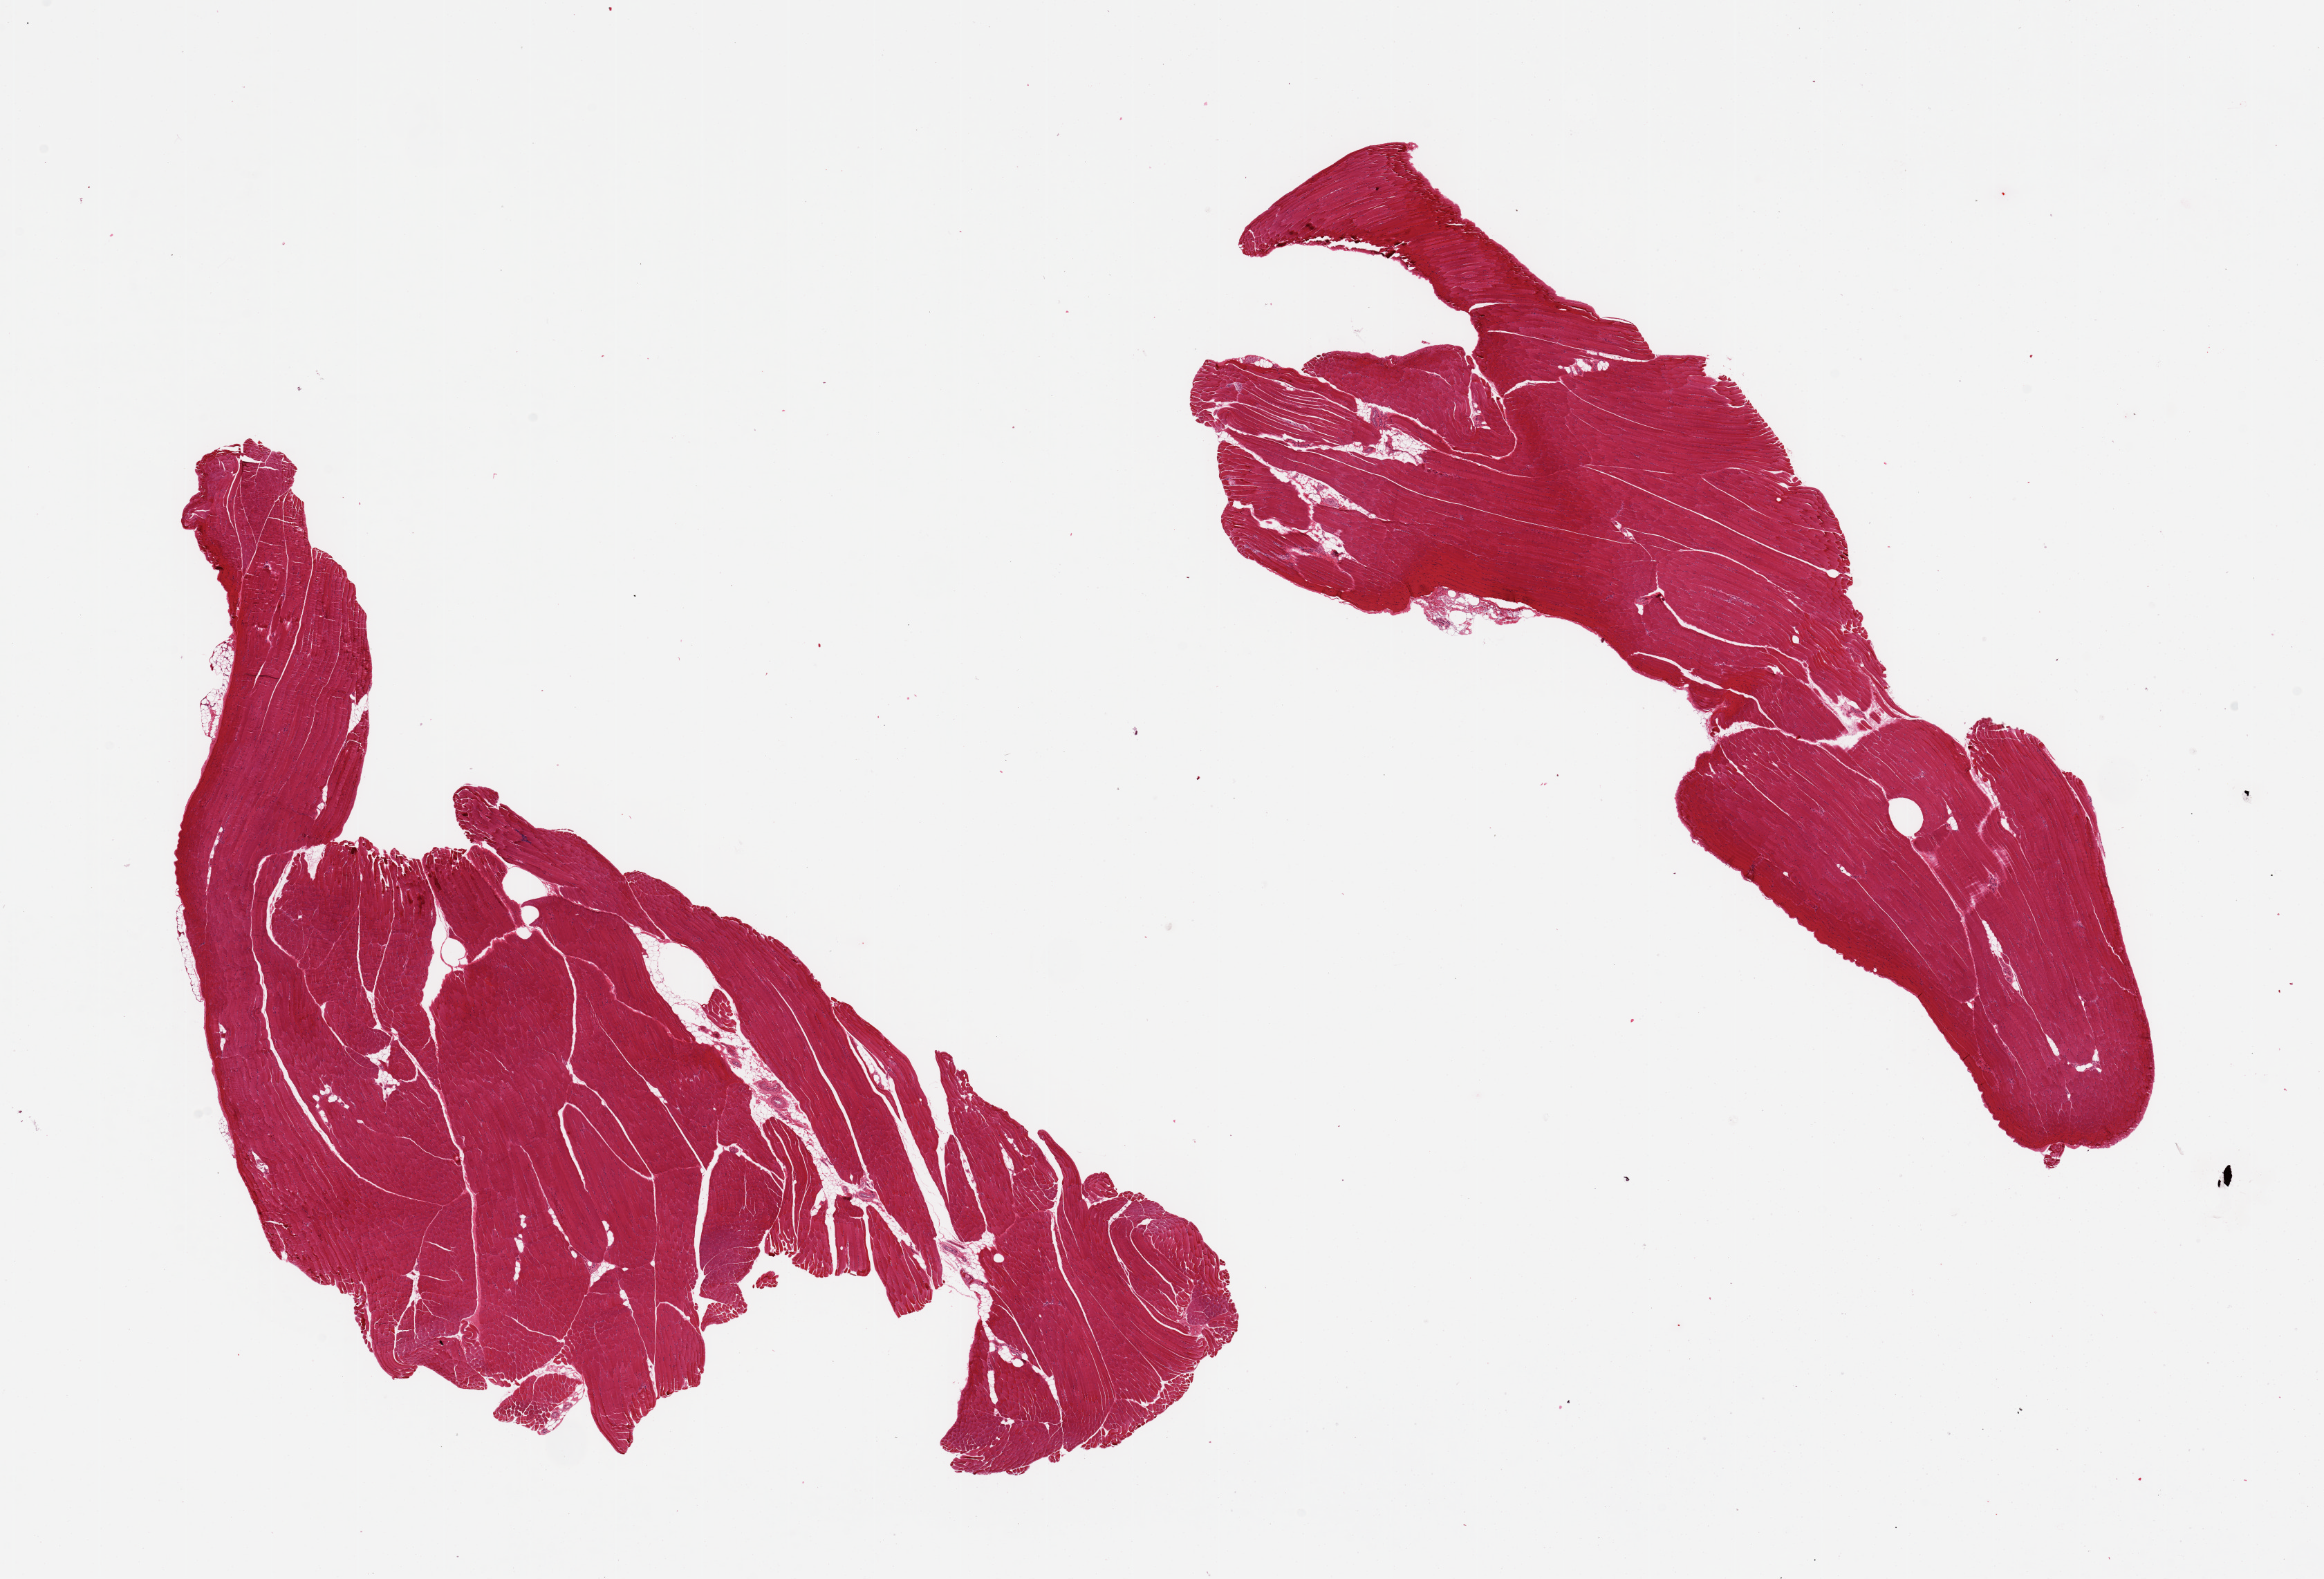
Digitized haematoxylin and eosin-stained section, shown as a low-resolution overview of the whole scanned area (about 26.6 x 18.1 mm), PAXgene-fixed, paraffin-embedded tissue, target tissue: skeletal muscle, tissue donor sample. Female donor.
- reviewer comment on this tissue sample: 2 pieces. No extraneous fat